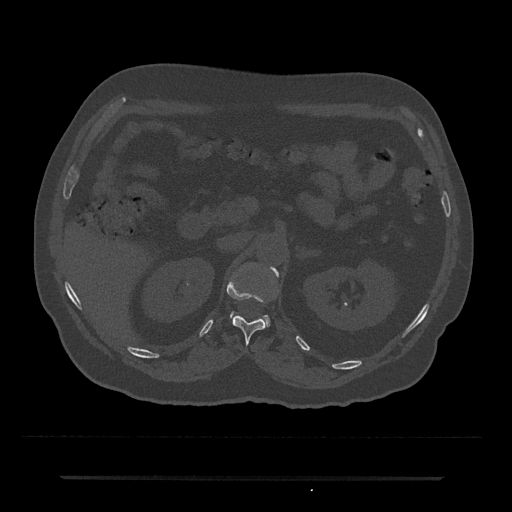
CT including the spine, one axial slice; slice 113 of 797 in the series (ordered by position); bone window (W 1800 / L 400 HU); 512 × 512 image matrix, field of view 437 × 437 mm. Male patient, age 69 years. From the clinical record (not read from this slice): primary cancer: prostate.
Annotated regions visible in this slice (semi-automatic segmentation, software-assisted and operator-edited):
- L1 vertebra: bounding box <262,267,279,325> (left, top, right, bottom; pixels)
- T12 vertebra: <227,271,278,344>